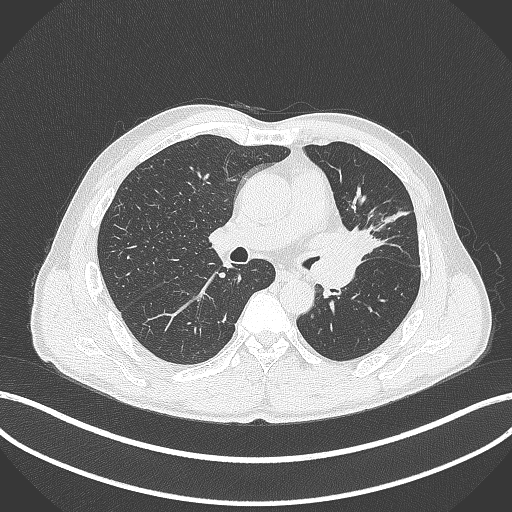
Chest CT, one axial slice; slice 242 of 429 in the series (ordered by position); reconstruction kernel B70f; lung window (W 1500 / L -600 HU); 1 mm slice thickness; 512 × 512 image matrix, field of view 400 × 400 mm. Male patient, age 57 years. Case-level facts recorded for this patient, not image findings: clinical TNM (as recorded): T2b N0 M0.
Annotated regions visible in this slice (rectangle marked by the reading radiologist):
- lung tumour (recorded histology: squamous cell carcinoma): box from (x=319, y=225) to (x=380, y=259) px